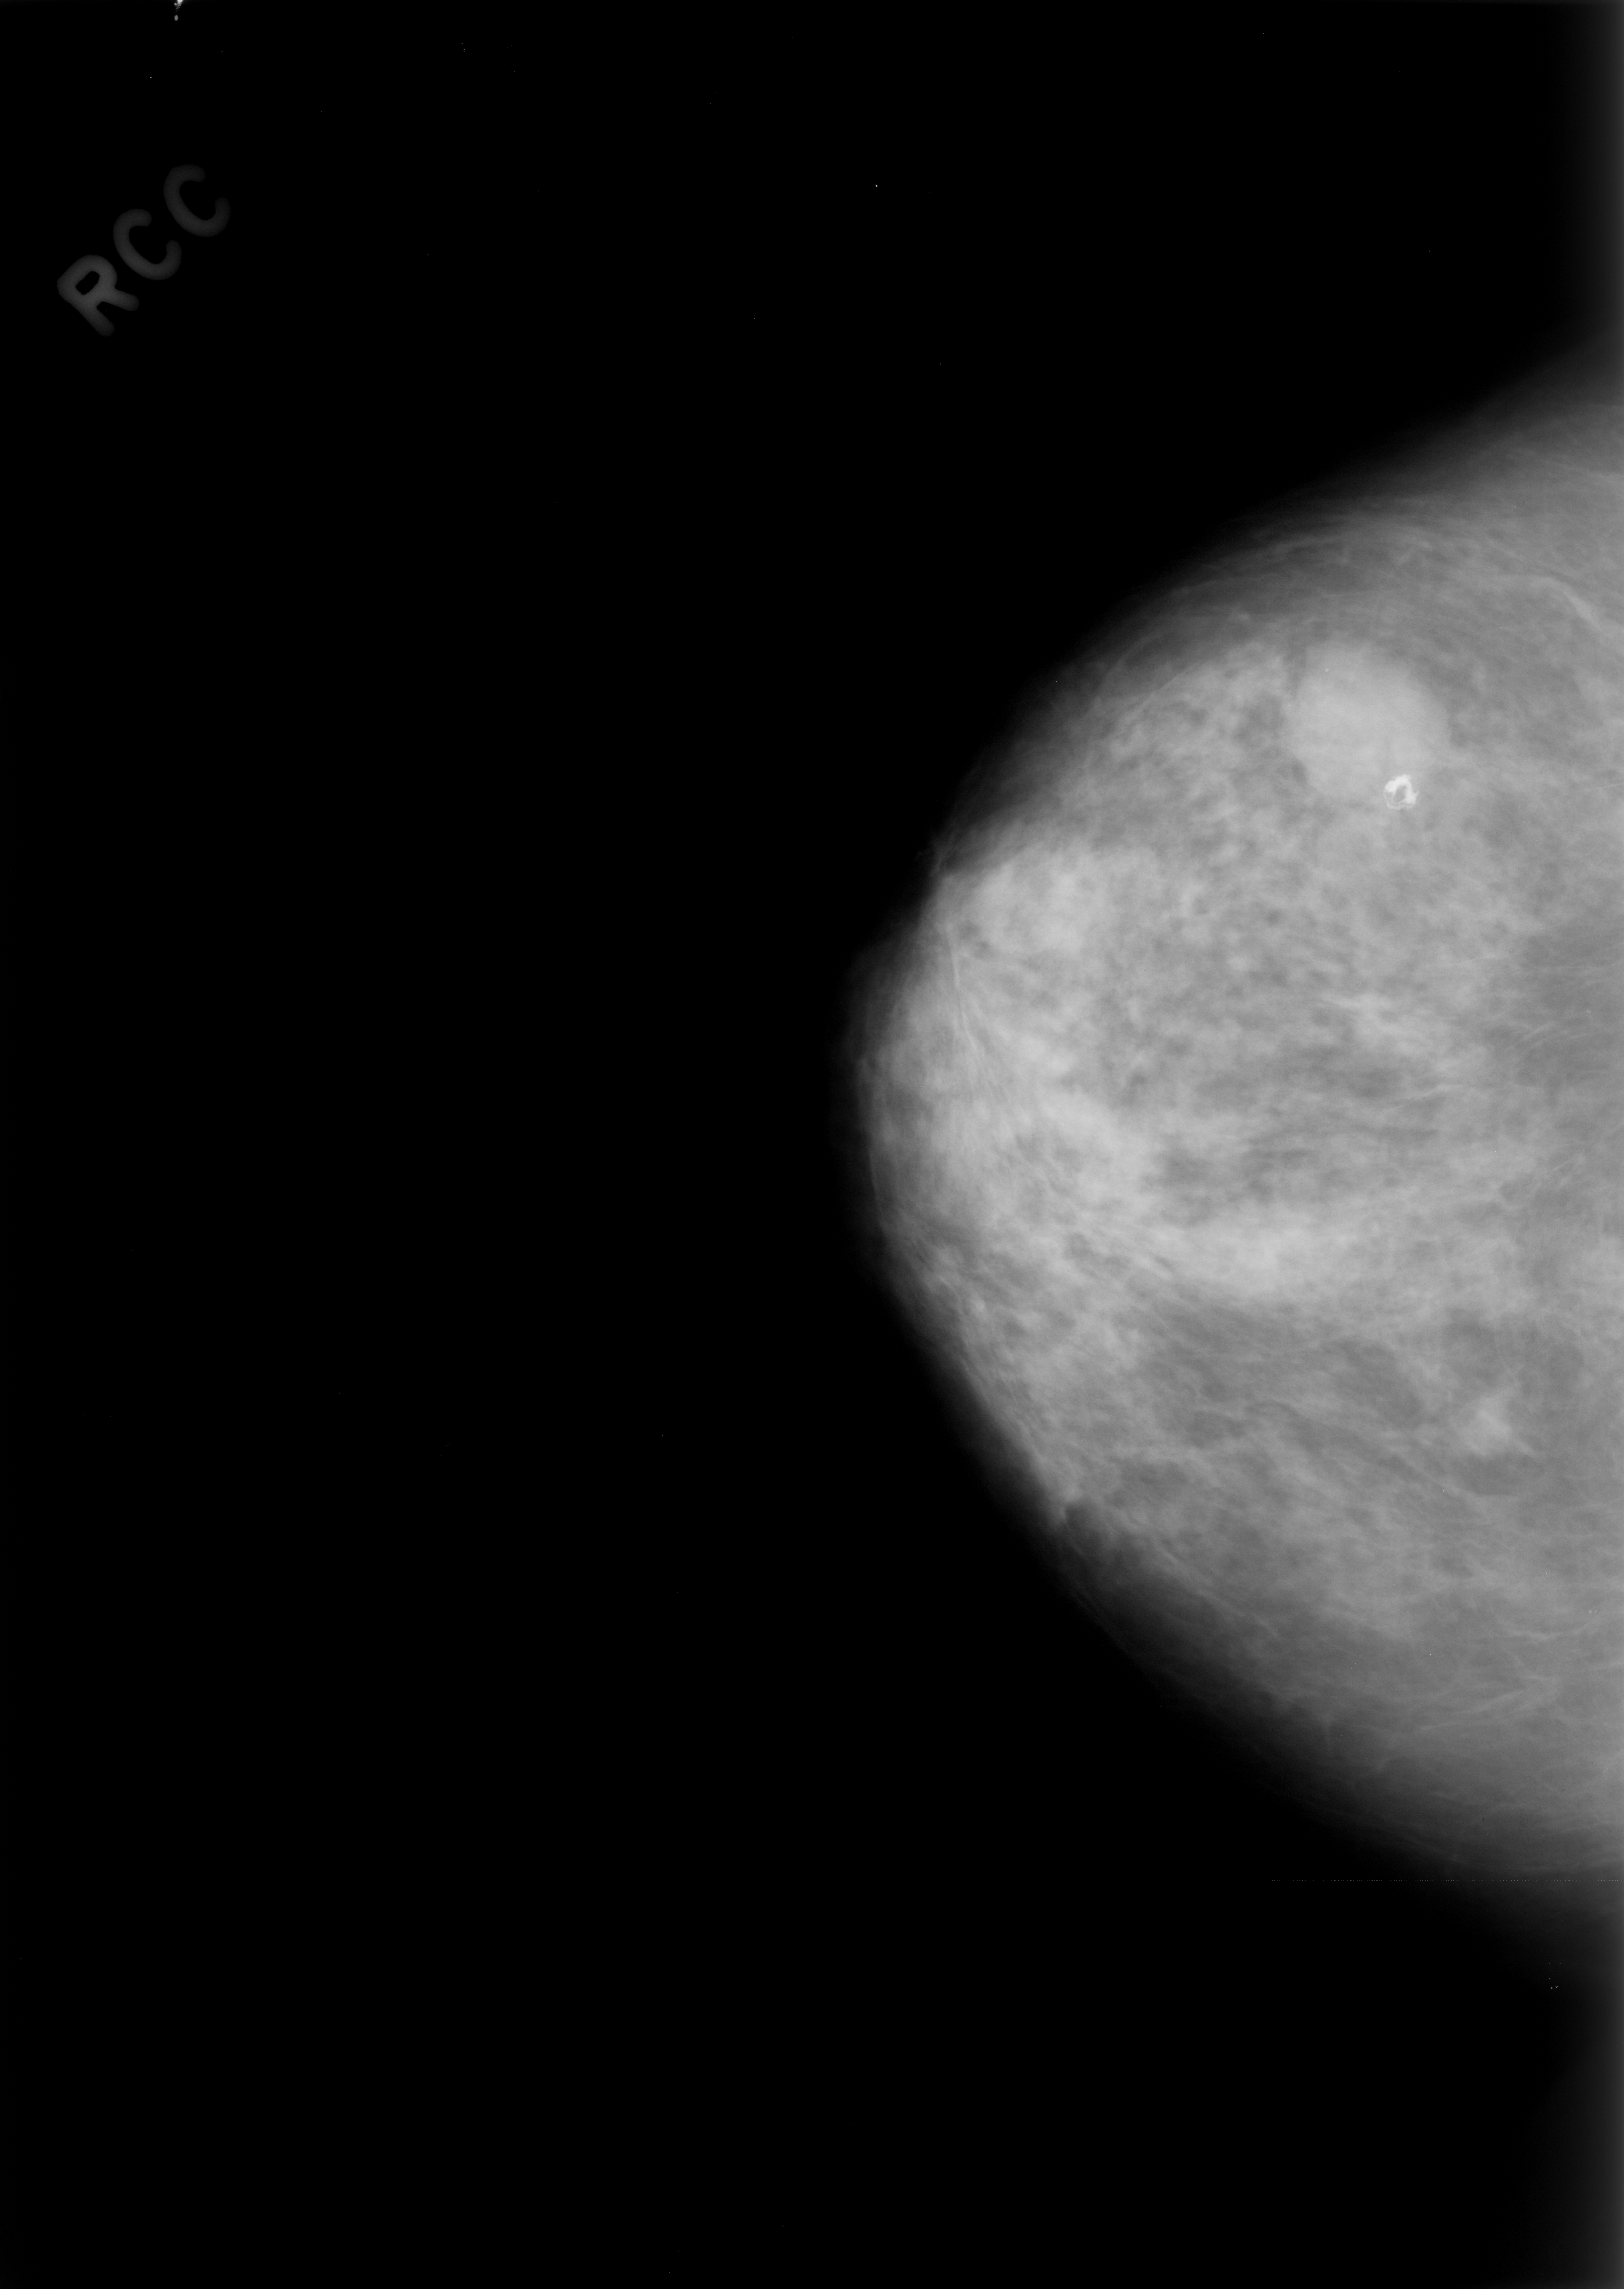
Scanned film-screen mammogram. Right breast. Craniocaudal (CC) view. Breast composition: scattered fibroglandular densities (BI-RADS density category 2 of 4). 1624 × 2289 image matrix.
Expert-marked regions of interest on this image (one box per marked abnormality):
- mass, shape round, margins microlobulated; BI-RADS assessment category 4; pathology result (as recorded, not read from the image): benign: bounding box [x1, y1, x2, y2] px = [1287, 643, 1430, 798]